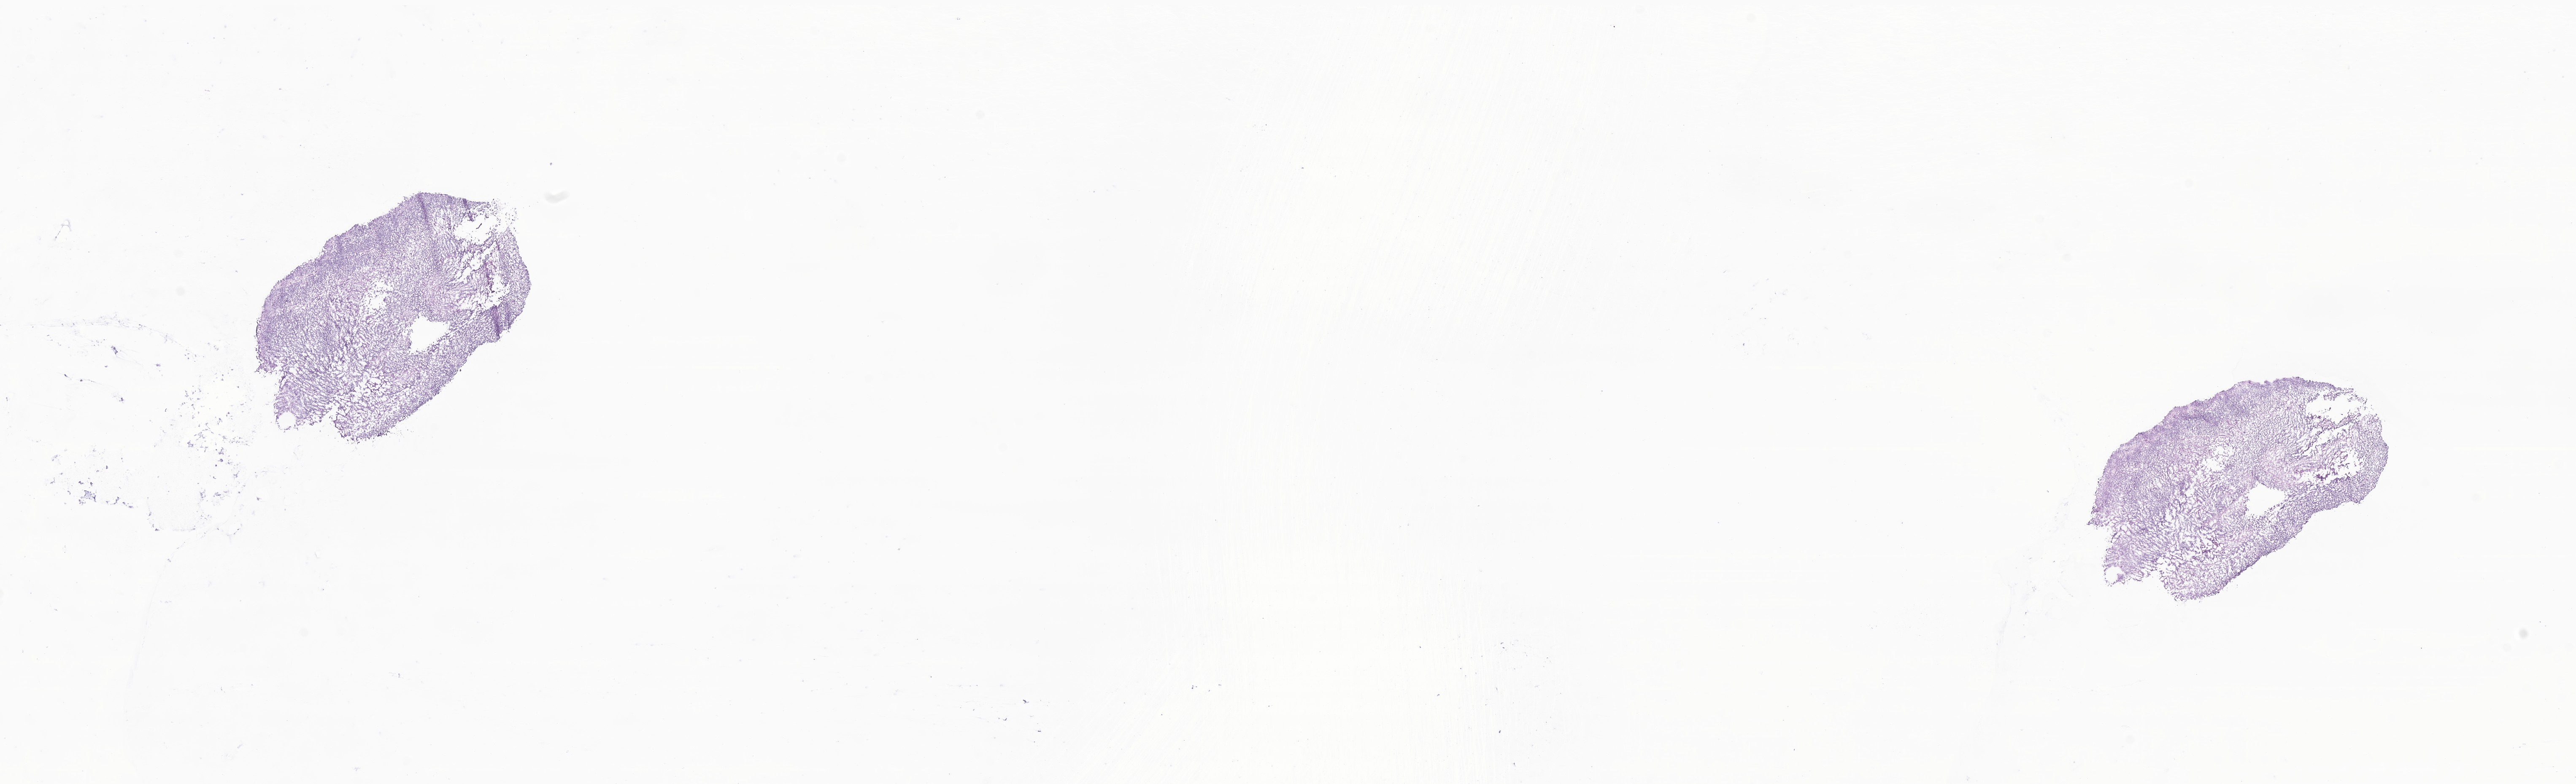
Whole-slide image, H&E stain of tumor tissue from the brain — a low-resolution overview of the entire scanned area, about 25.7 x 7.8 mm. Frozen section (OCT-embedded). Female patient, age 252 months (21 years).
Recorded diagnosis: Ganglioglioma, NOS.